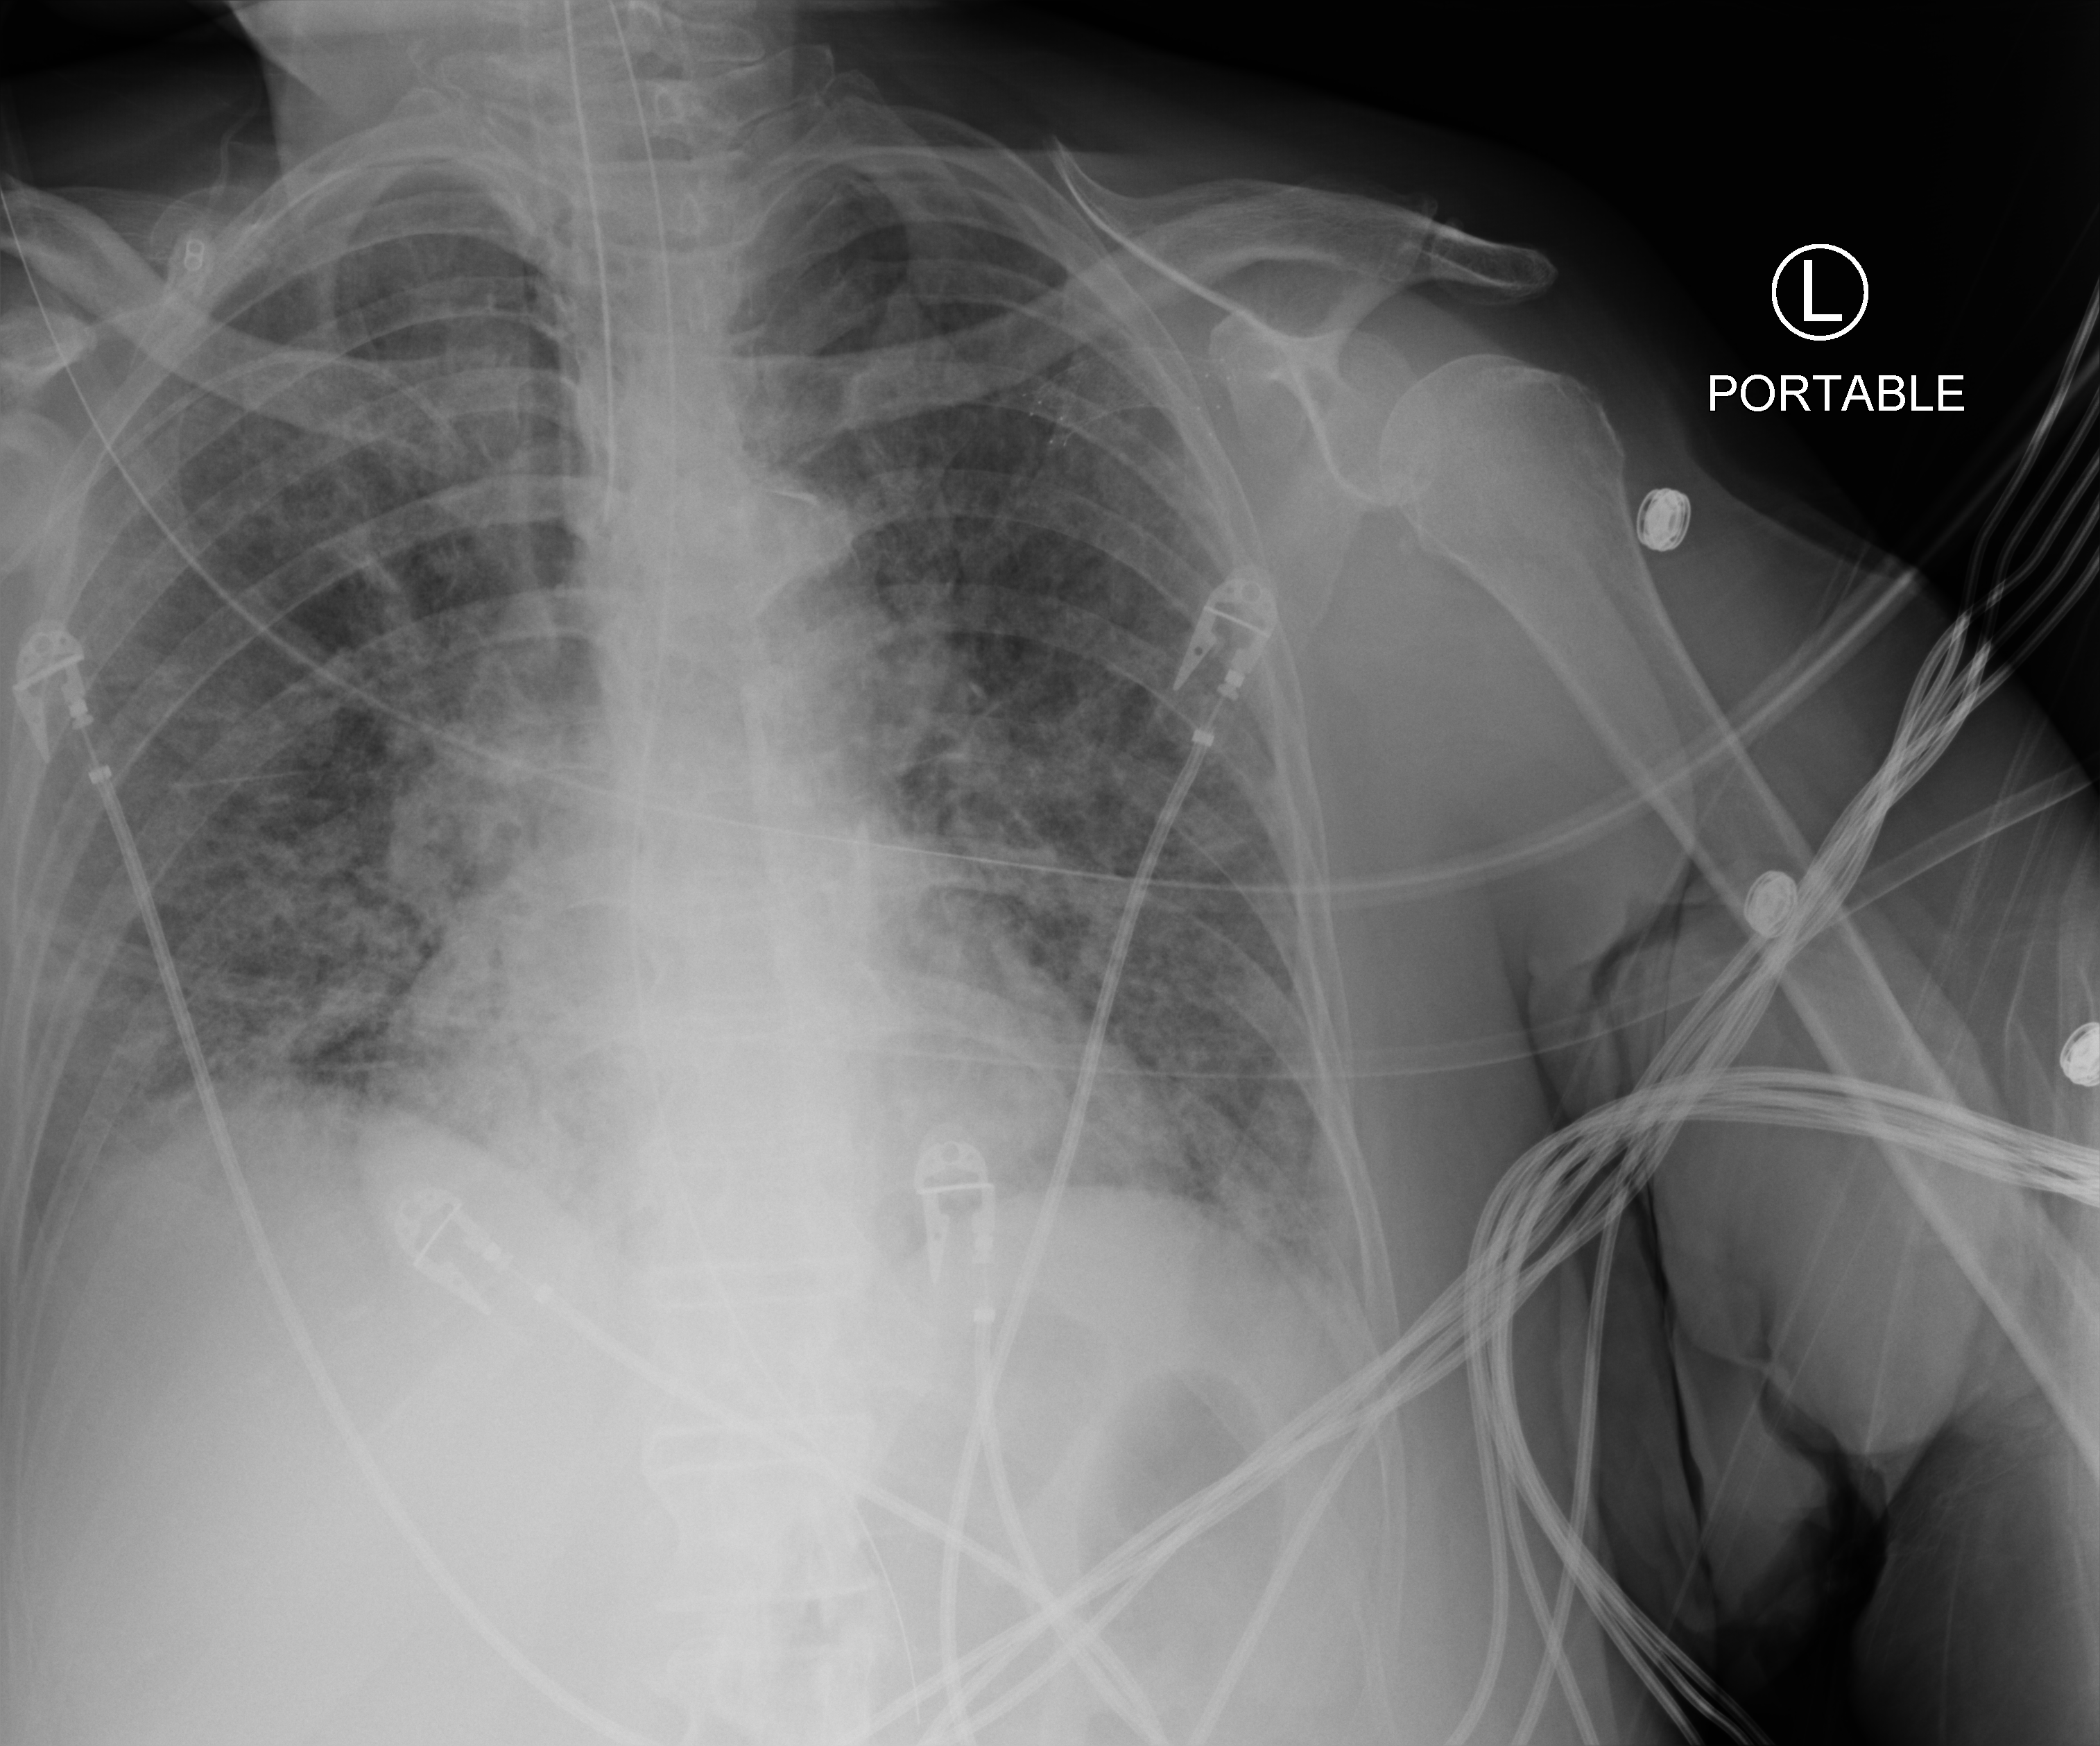
Portable chest radiograph, anteroposterior (AP) projection. Female patient hospitalised with COVID-19, age 60–74 years.
From the hospital-stay record, not from the radiograph (when in the stay this image was taken is not recorded): length of hospital stay: 23 days.